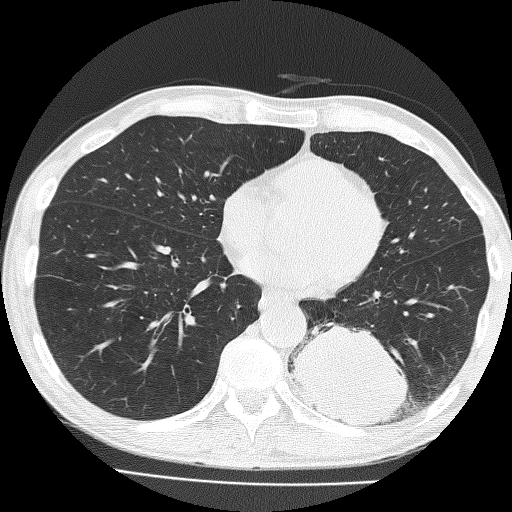
Low-dose screening chest CT, one axial slice; slice 65 of 160 in the series (ordered by position); 120 kVp; lung window (W 1500 / L -600 HU); 512 × 512 image matrix.
Annotated regions visible in this slice (expert manual segmentation):
- lesion 1 (tumor, lower lobe of left lung): bounding box <291,323,408,426> (left, top, right, bottom; pixels)